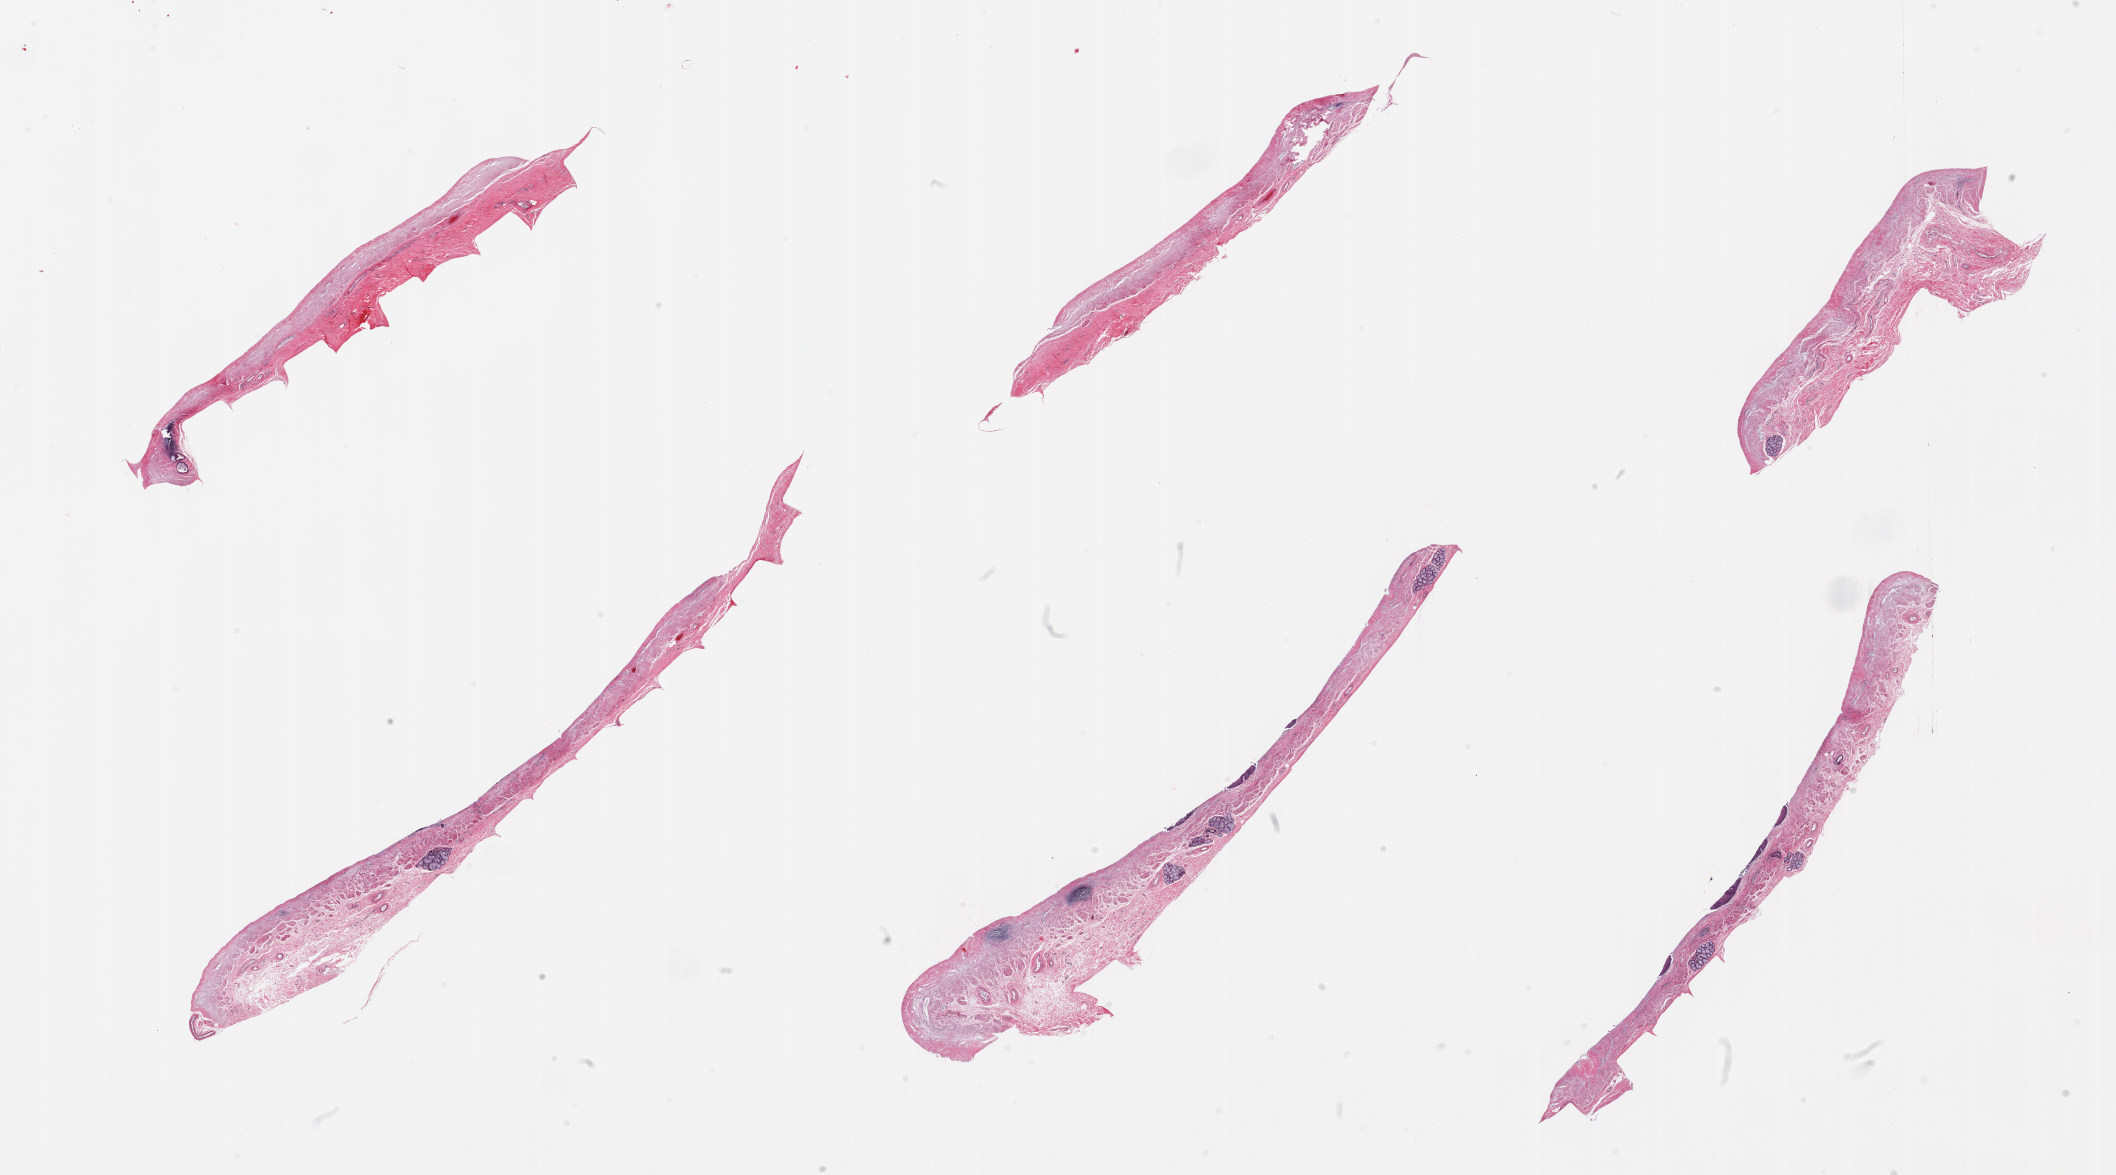
Whole-slide image, H&E stain, whole scanned area (about 33.5 x 18.6 mm) shown as a low-resolution overview. PAXgene-fixed, paraffin-embedded tissue. Target tissue: esophageal mucous membrane. Donor tissue sample. Donor sex: male.
• review note (as recorded): 6 pieces; minimal residual squamous epithelium